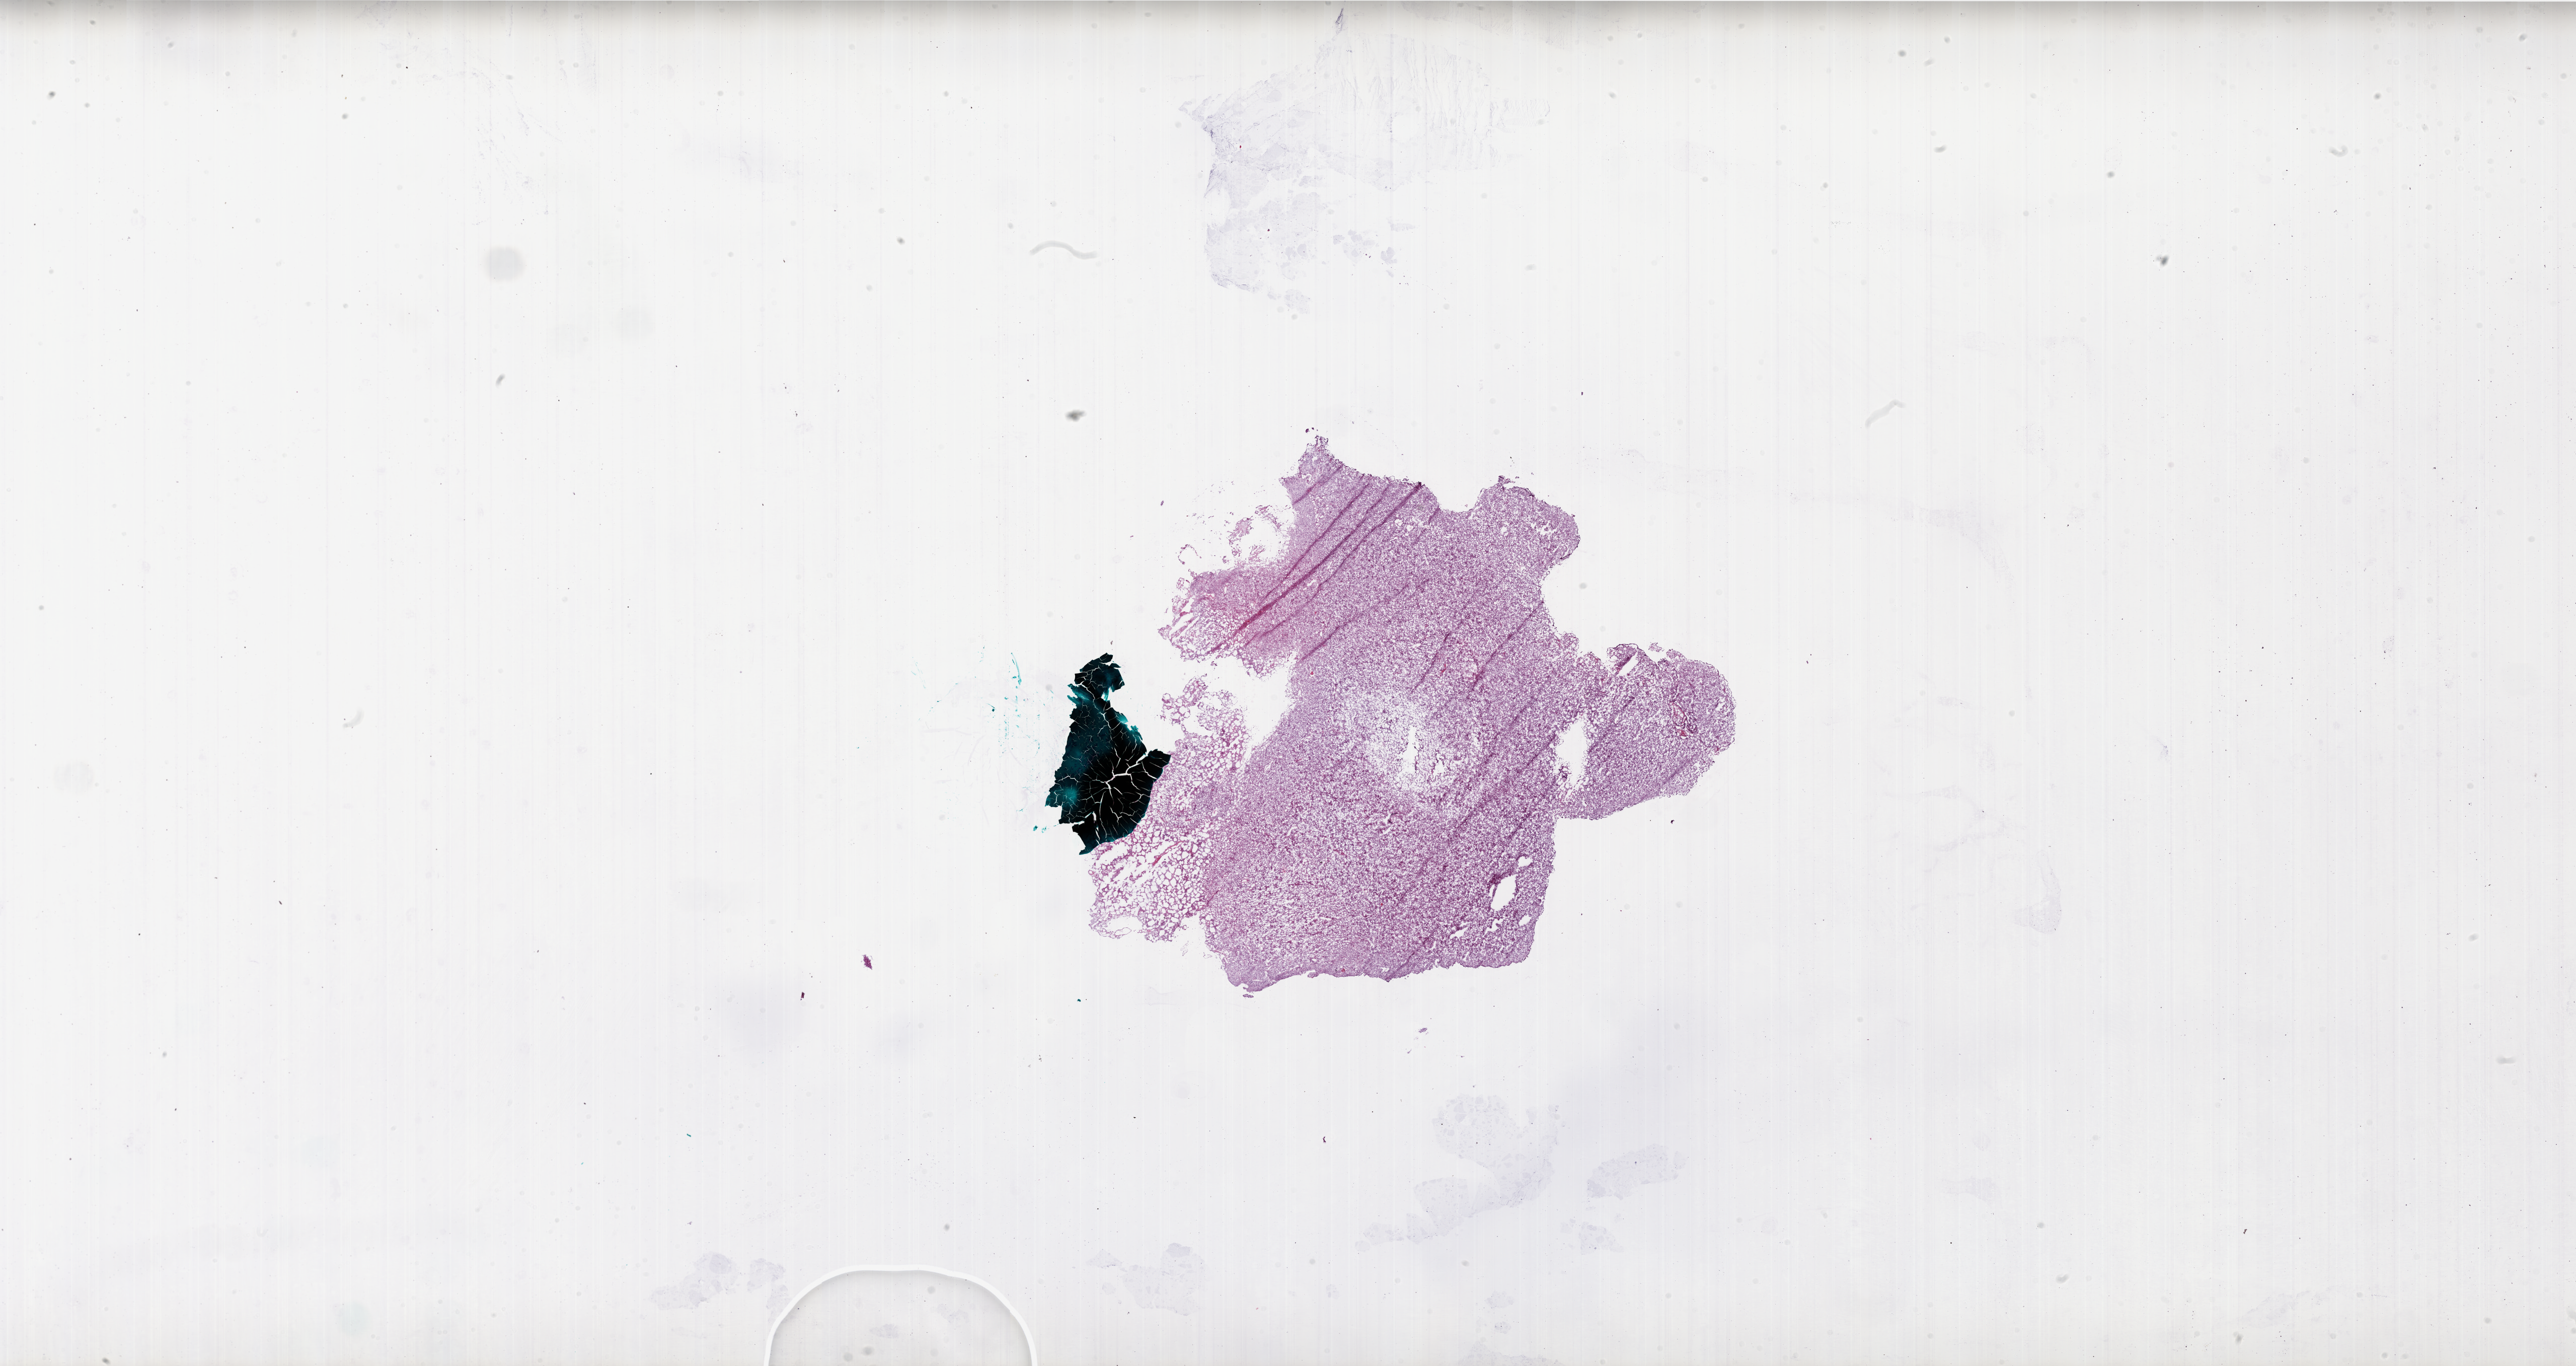
Whole-slide histology image, H&E-stained — low-resolution overview of the scanned area, about 41.0 x 21.7 mm (acquisition: 20x scan); frozen section; sample: primary tumour, brain. Male patient; age at initial diagnosis 54 years. Slide review estimates, as recorded: tumour cells 80%, tumour nuclei 90%, normal cells 0%, stromal cells 5%, necrosis 15%.
• histologic diagnosis: Glioblastoma